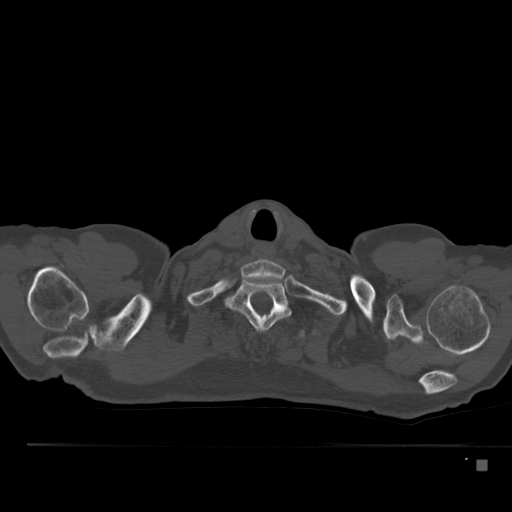
CT including the spine, one axial slice. 120 kVp. Bone window (W 1800 / L 400 HU). 512 × 512 image matrix. Male patient, age 70 years. From the clinical record (not read from this slice): primary cancer: renal.
Annotated regions visible in this slice (semi-automatically segmented with operator editing):
- T1 vertebra: bounding box <229,279,291,330> (left, top, right, bottom; pixels)
- T2 vertebra: <271,308,305,340>